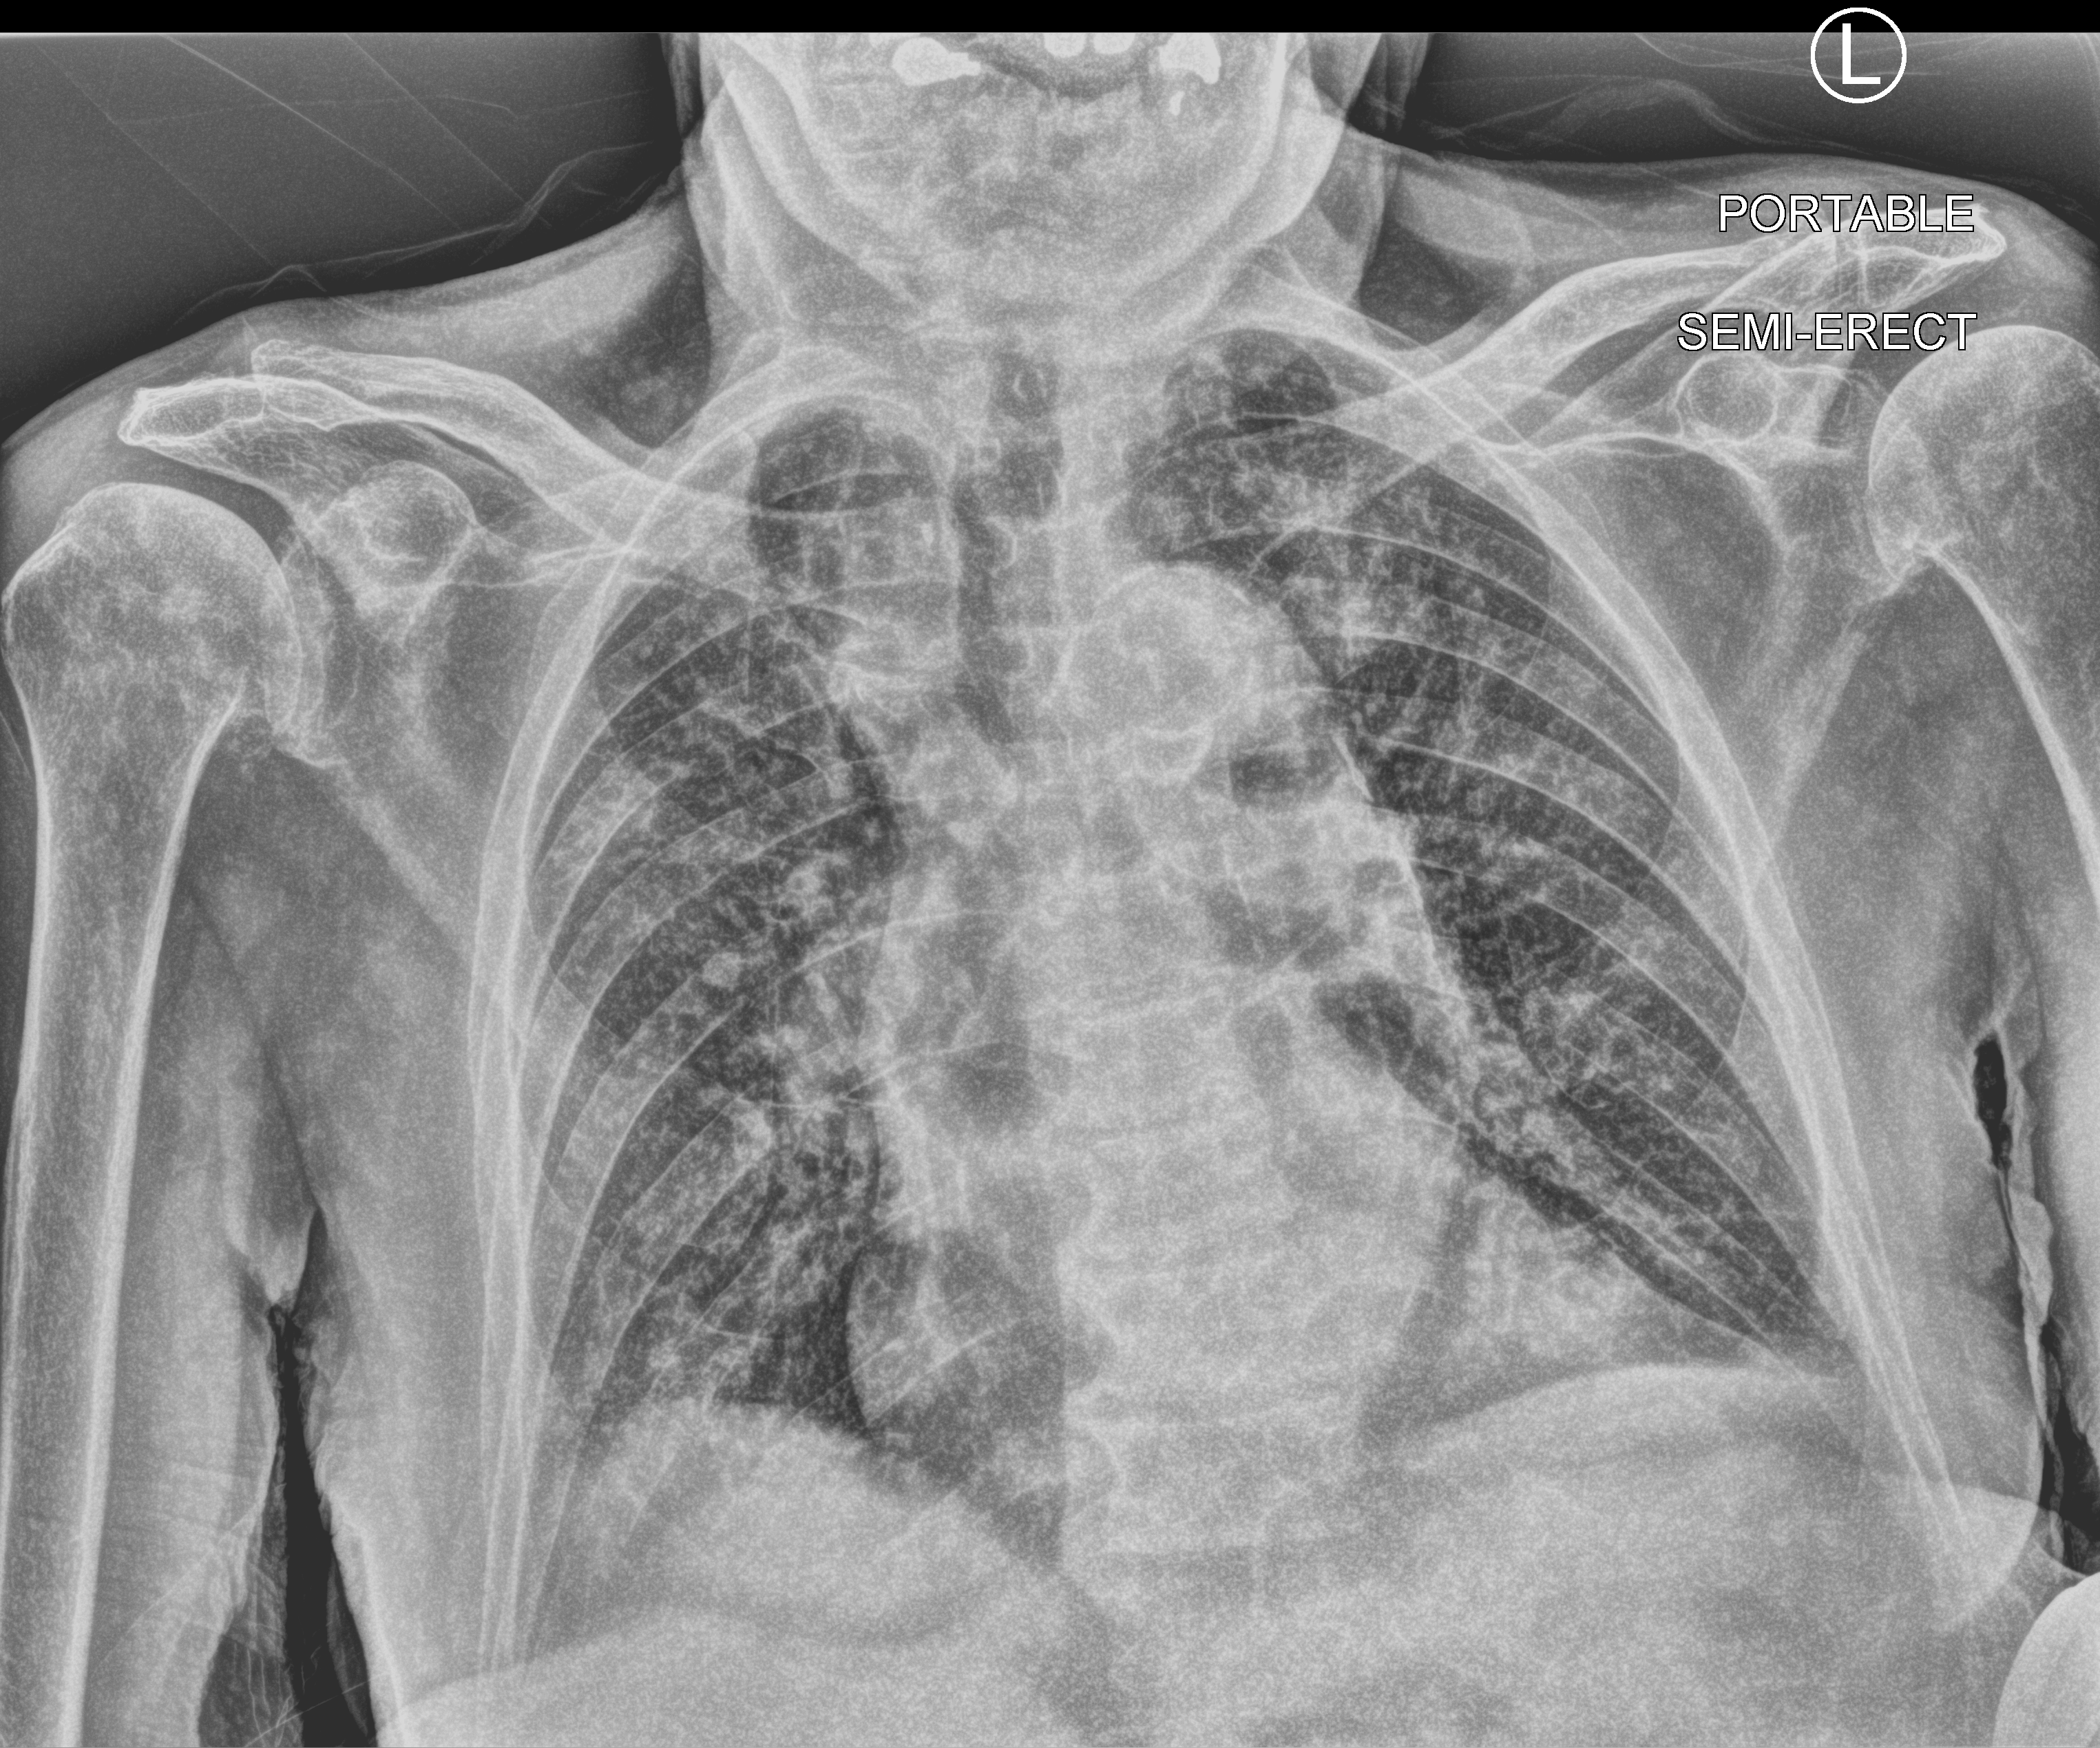
Portable chest radiograph, anteroposterior (AP) projection. Patient hospitalised with COVID-19; male, aged 75–90 years.
Admission-level facts for this patient (not findings on this image; timing relative to this image not recorded): mechanically ventilated during this hospital stay: no.